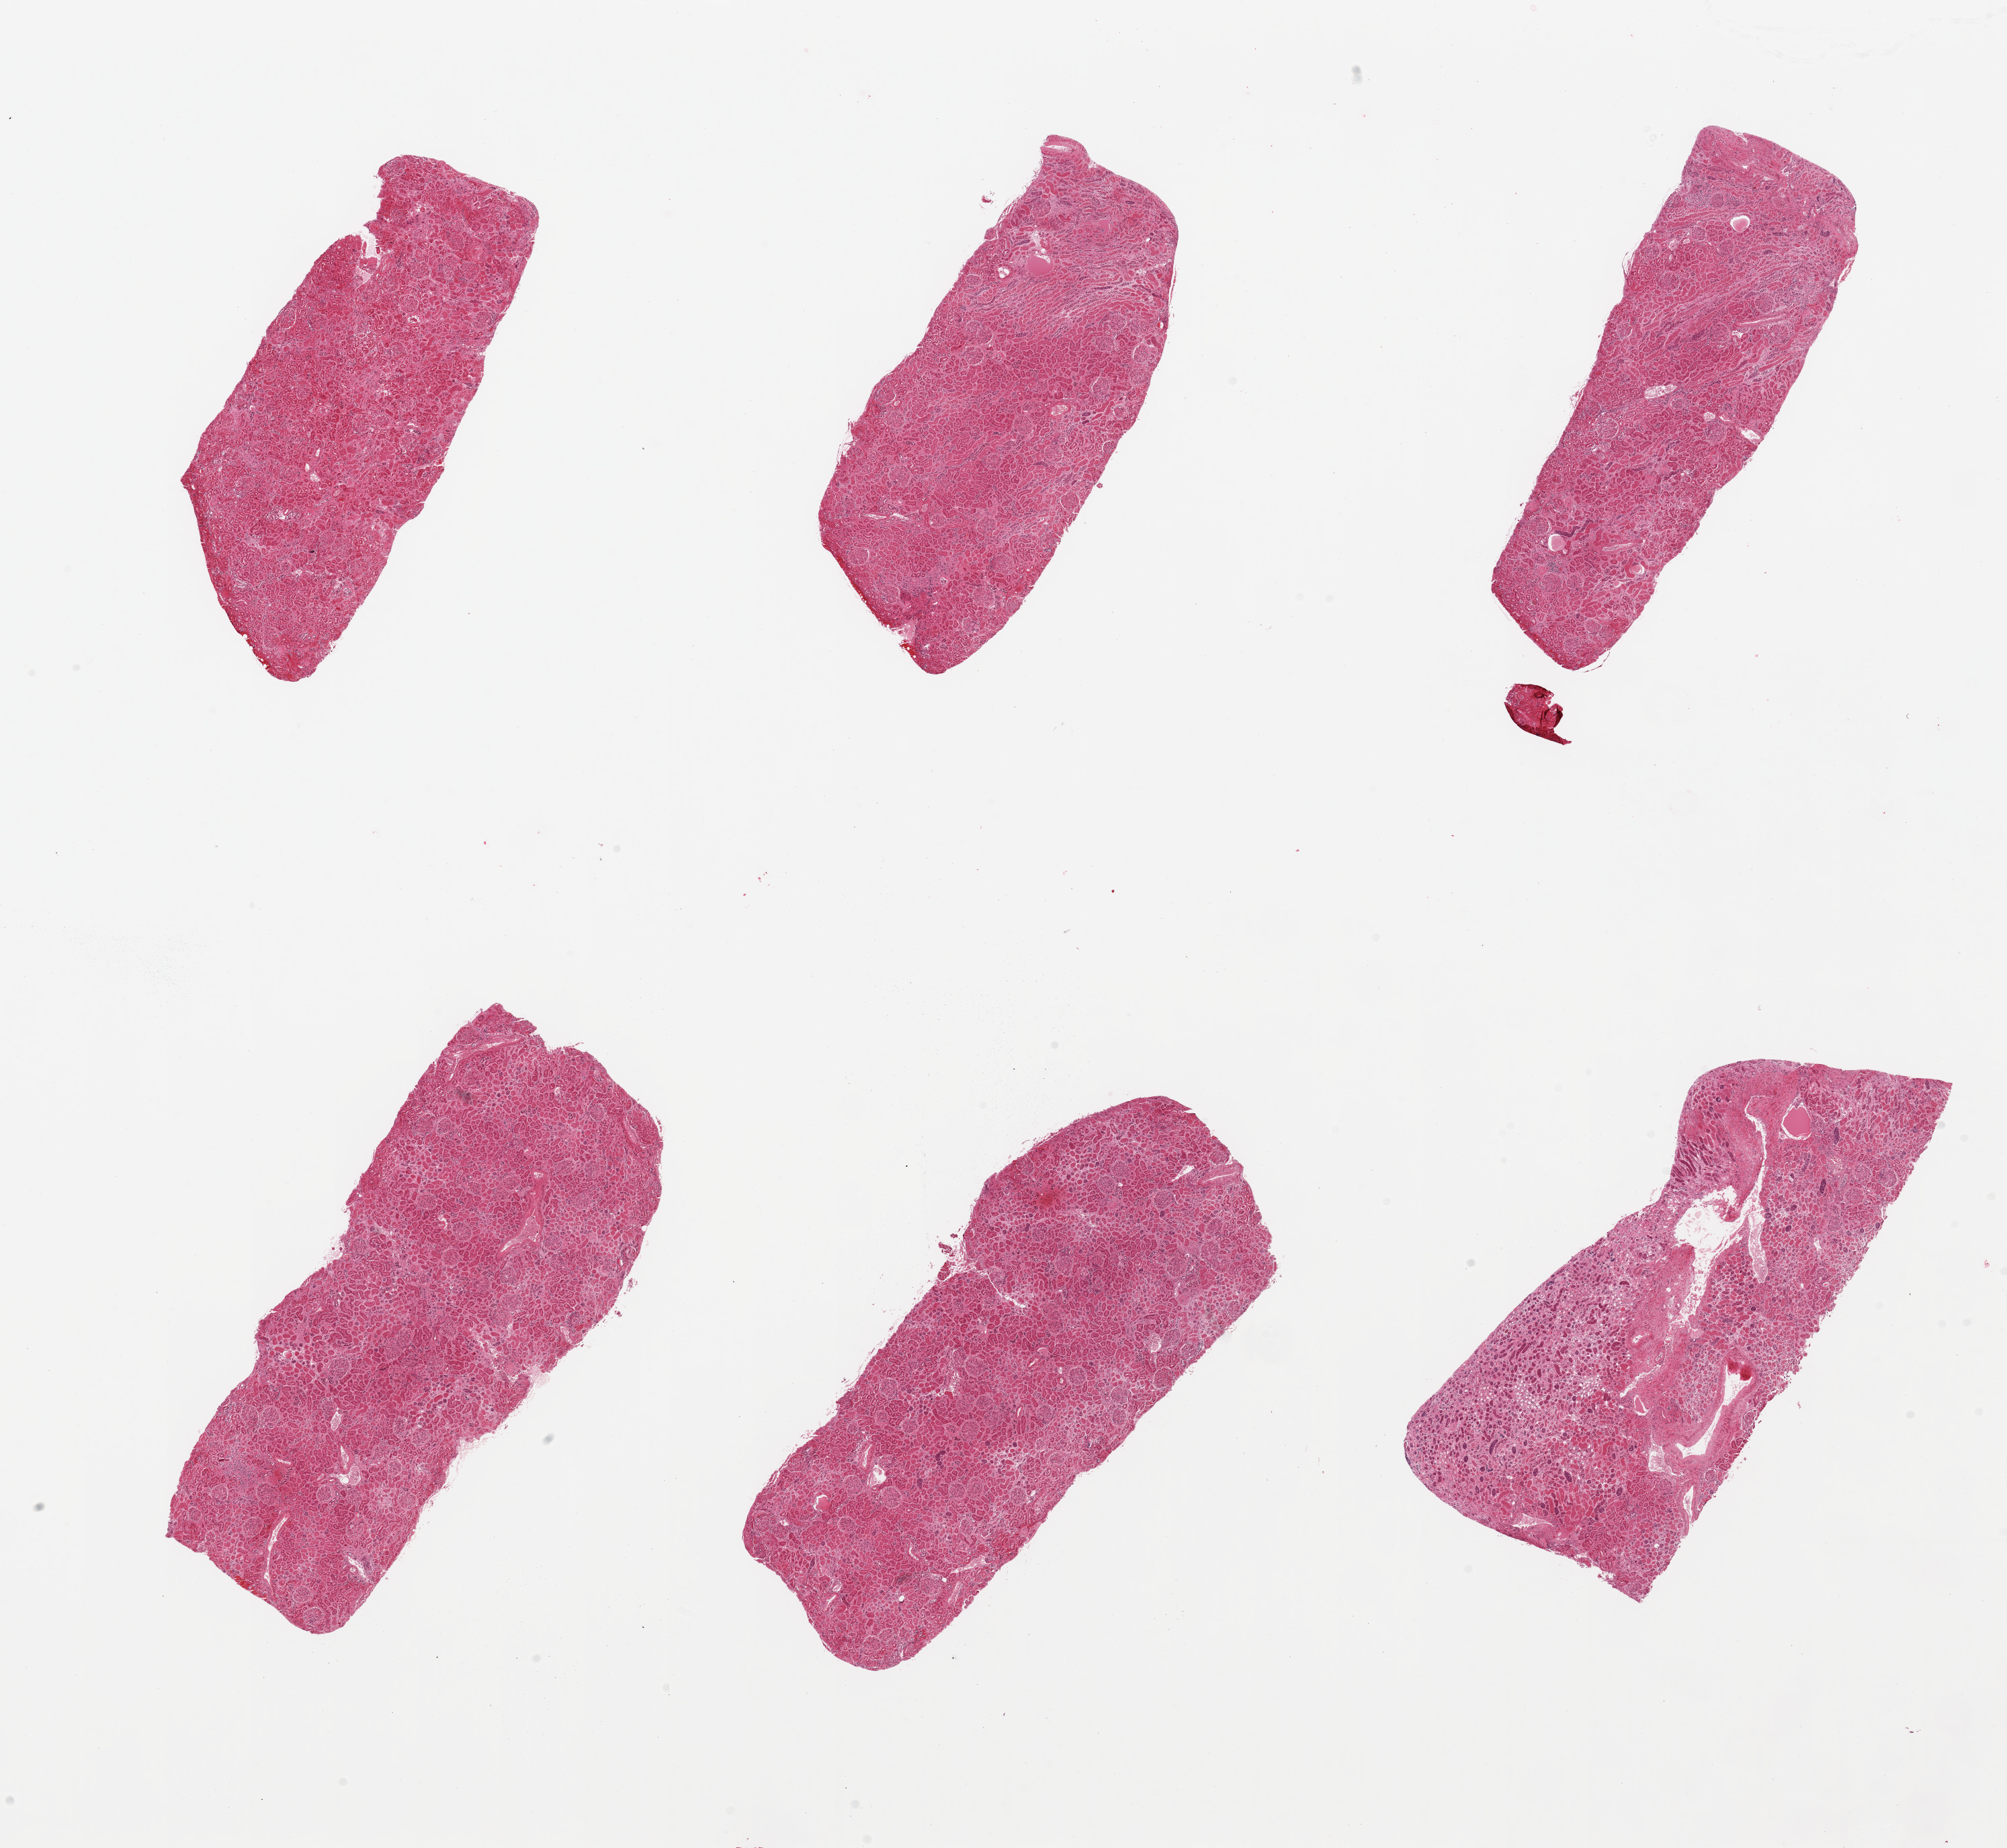
Digitized H&E-stained section, brightfield, shown as a low-resolution overview of the whole scanned area (about 23.6 x 21.8 mm); PAXgene-fixed paraffin-embedded (PFPE) section; sampled site (target tissue): renal cortex; donor tissue sample. Female donor.
- review note (as recorded): 6 pieces; glomeruli in all sections, portion of medulla, some vascular thickening, rare sclerotic glomerulus